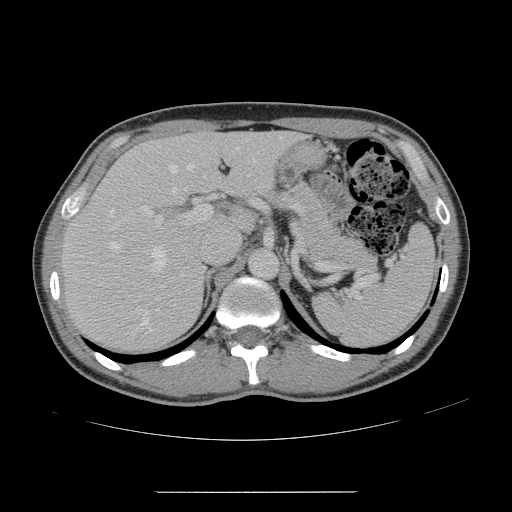
Contrast-enhanced abdominal CT, one axial slice; position 99 of 178 along the scan axis; intravenous contrast given; soft-tissue window (W 400 / L 40 HU); 512 × 512 image matrix, field of view 401 × 401 mm. Male patient, age 53 years. Case-level facts recorded for this patient, not image findings: diagnosis: colorectal cancer liver metastases, imaged before liver resection; multiple liver metastases: yes; largest metastasis: 2.4 cm; disease in both lobes: no.
Annotated regions visible in this slice (expert manual segmentation):
- hepatic veins: box from (x=110, y=147) to (x=238, y=325) px
- liver: (x=63, y=133)–(x=299, y=349)
- planned liver remnant (the part of the liver to remain after resection): (x=147, y=134)–(x=298, y=227)
- portal vein (with intrahepatic branches): (x=140, y=205)–(x=212, y=227)